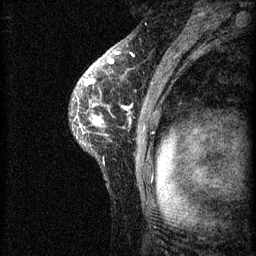
Breast MRI (dynamic contrast-enhanced), one sagittal slice. Position 48 of 60 along the scan axis. 3 images stored at this slice position (order not interpretable as contrast timing). 1.5 T. TE 4.2 ms, TR 8.2 ms. 256 × 256 image matrix, field of view 180 × 180 mm. Patient: female, 41 years.
Annotated regions visible in this slice (semi-automatic segmentation, software-assisted and operator-edited):
- analysis volume of interest (the breast-tissue region the enhancement analysis was run in; not a lesion): bounding box (x1, y1, x2, y2) in pixels: (70, 62, 160, 175)
- tumour enhancement mask (voxels above the 70 % enhancement threshold inside the analysis volume of interest): (75, 62, 132, 135)